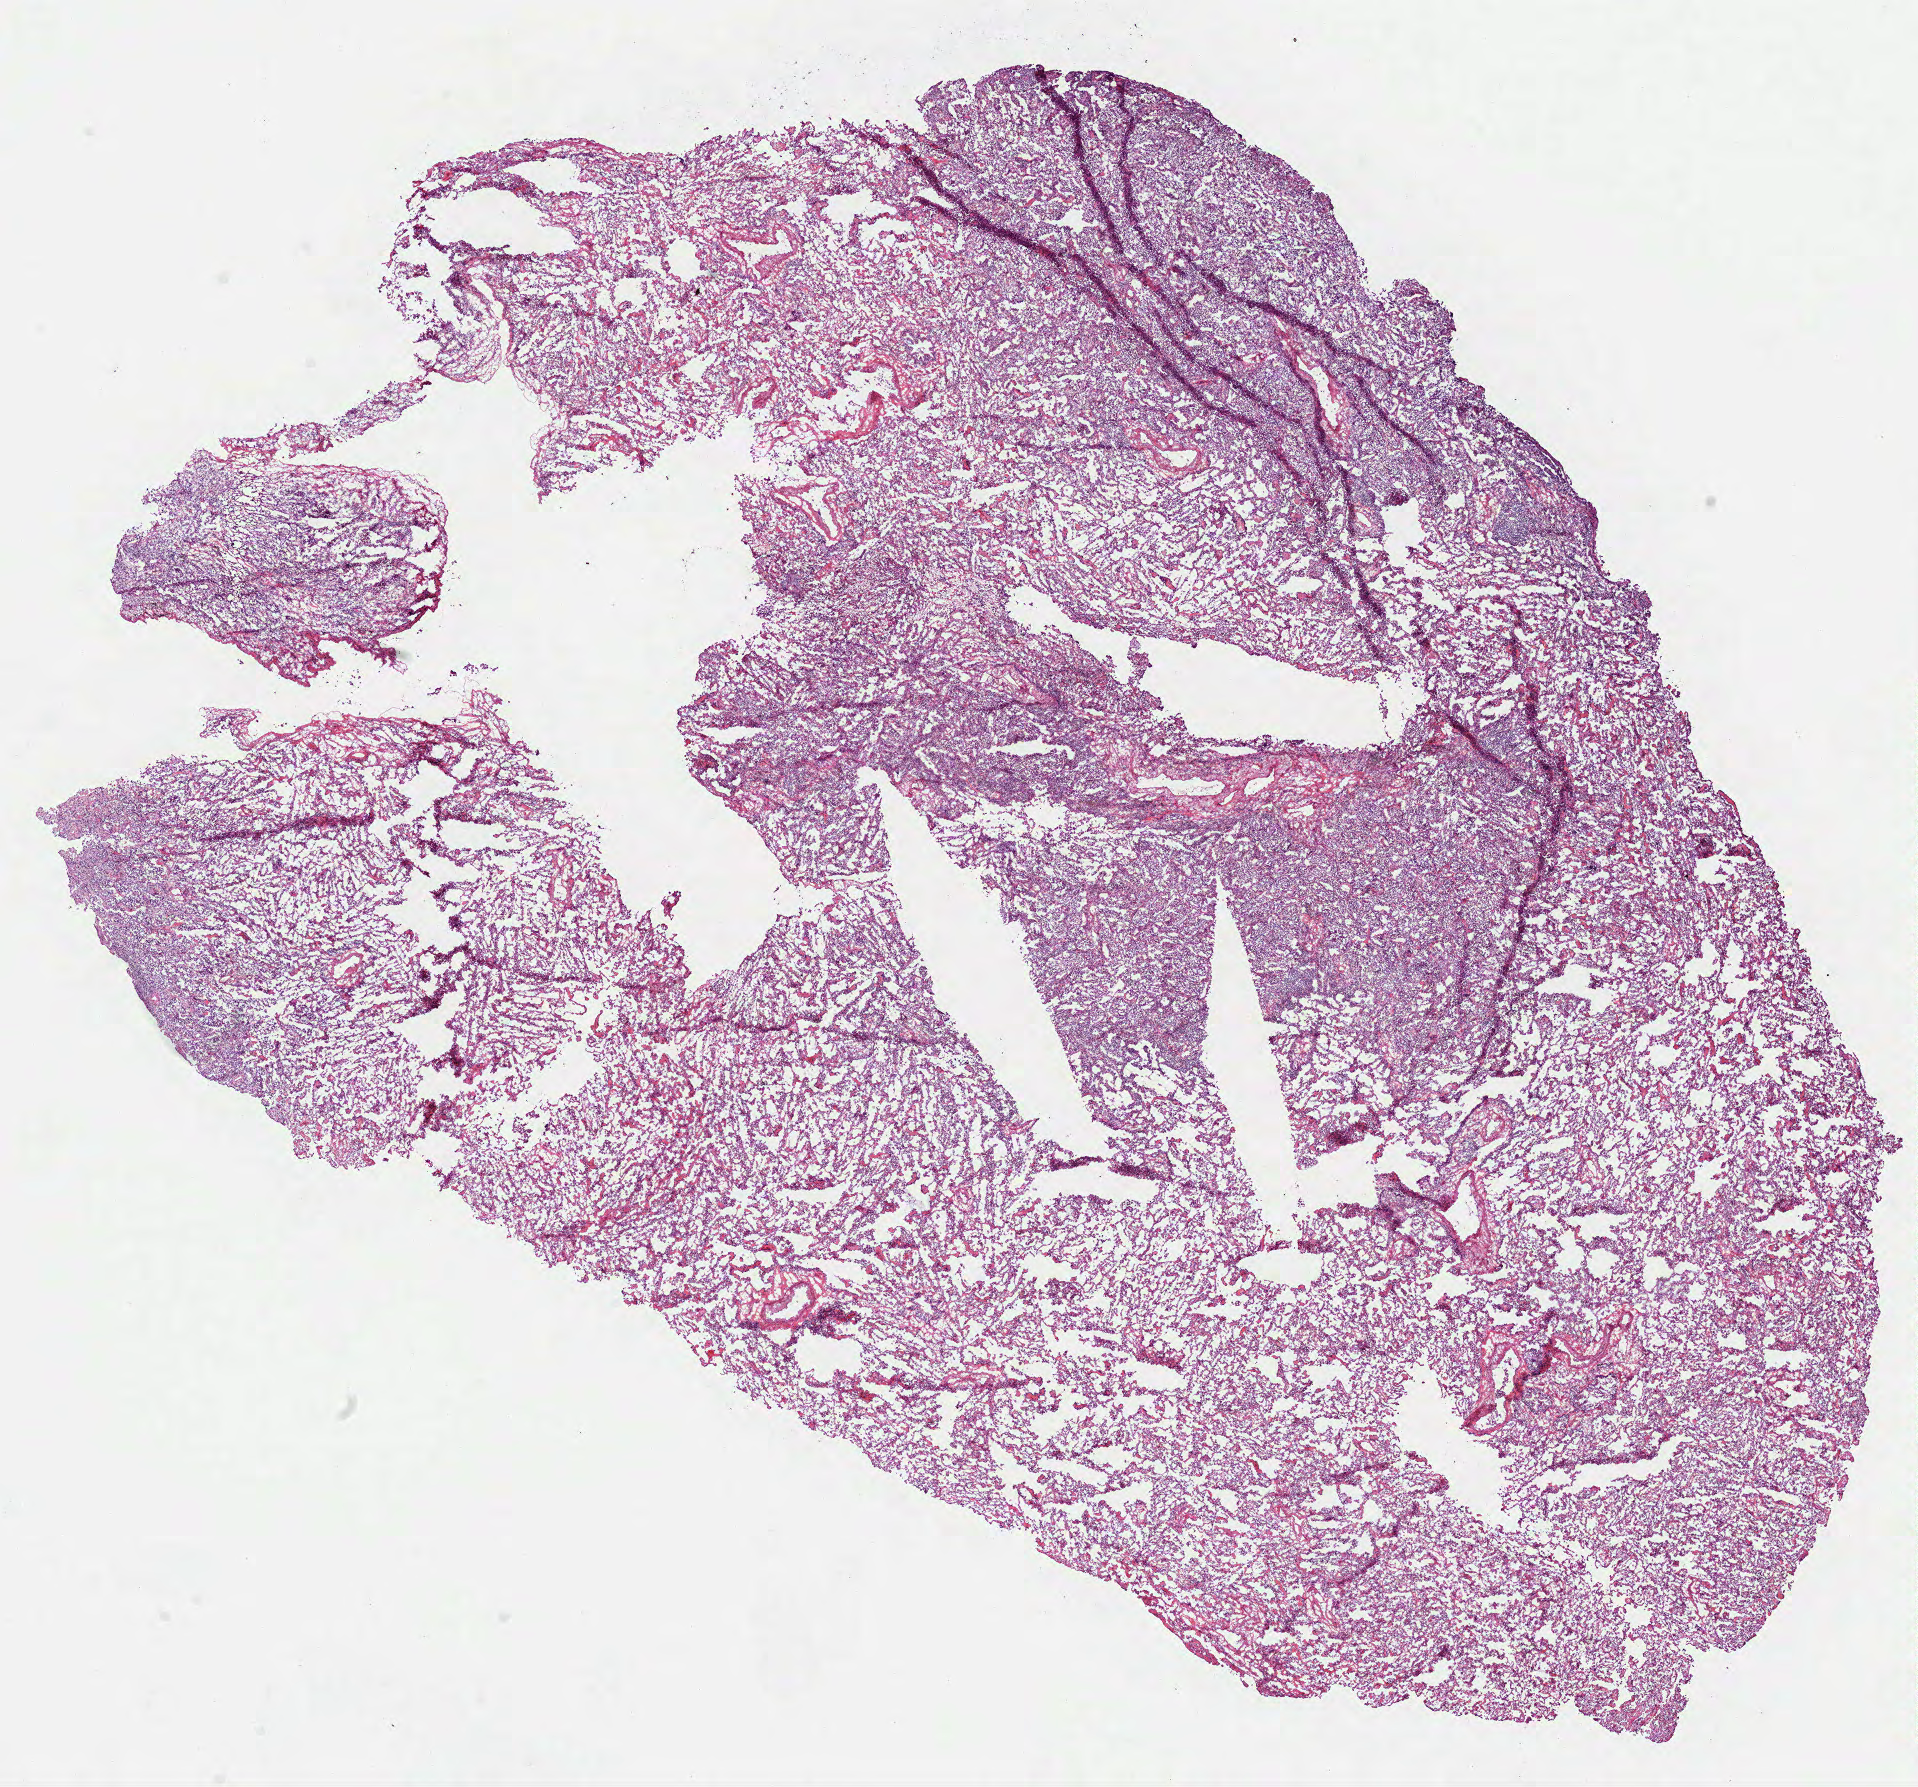
H&E whole-slide image — a low-resolution overview of the entire scanned area, about 15.5 x 14.4 mm (from a 40x scan). Frozen section. Sample: primary tumour, lung. Female patient; age at initial diagnosis 58 years. Slide review estimates, as recorded: tumour cells 90%, tumour nuclei 65%, normal cells 10%, necrosis 0%. Infiltration values recorded for this section: lymphocyte infiltration 10%, monocyte infiltration 10%.
Diagnosis: Bronchiolo-alveolar carcinoma, non-mucinous (lower lobe, lung). AJCC pathologic stage: IA (6th edition).